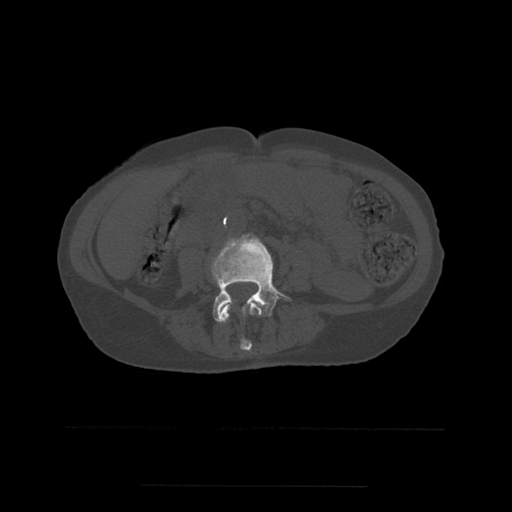
CT including the spine, one axial slice; position 174 of 544 along the scan axis; bone window (W 1800 / L 400 HU); 1.25 mm slice thickness; 512 × 512 image matrix, field of view 350 × 350 mm. Patient age 58 years. Case-level facts recorded for this patient, not image findings: primary cancer: lung.
Annotated regions visible in this slice (semi-automatic segmentation, software-assisted and operator-edited):
- L3 vertebra: bounding box (x1, y1, x2, y2) in pixels: (218, 297, 263, 351)
- L4 vertebra: (212, 234, 292, 322)